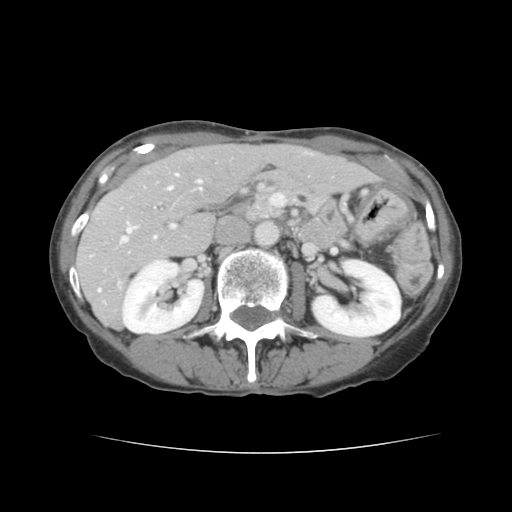
Contrast-enhanced abdominal CT, one axial slice. Position 66 of 136 along the scan axis. 120 kVp. Intravenous contrast given. Soft-tissue window (W 400 / L 40 HU). 2.5 mm slice thickness. 512 × 512 image matrix, field of view 319 × 319 mm. Female patient, age 77 years. From the clinical record (not read from this slice): diagnosis: colorectal cancer liver metastases, imaged before liver resection; multiple liver metastases: yes; largest metastasis: 3 cm; disease in both lobes: no.
Outlined on this slice (expert manual segmentation):
- hepatic veins: bounding box [x1, y1, x2, y2] px = [122, 174, 202, 242]
- liver: [78, 145, 375, 327]
- planned liver remnant (the part of the liver to remain after resection): [160, 145, 375, 206]
- portal vein (with intrahepatic branches): [98, 224, 175, 292]